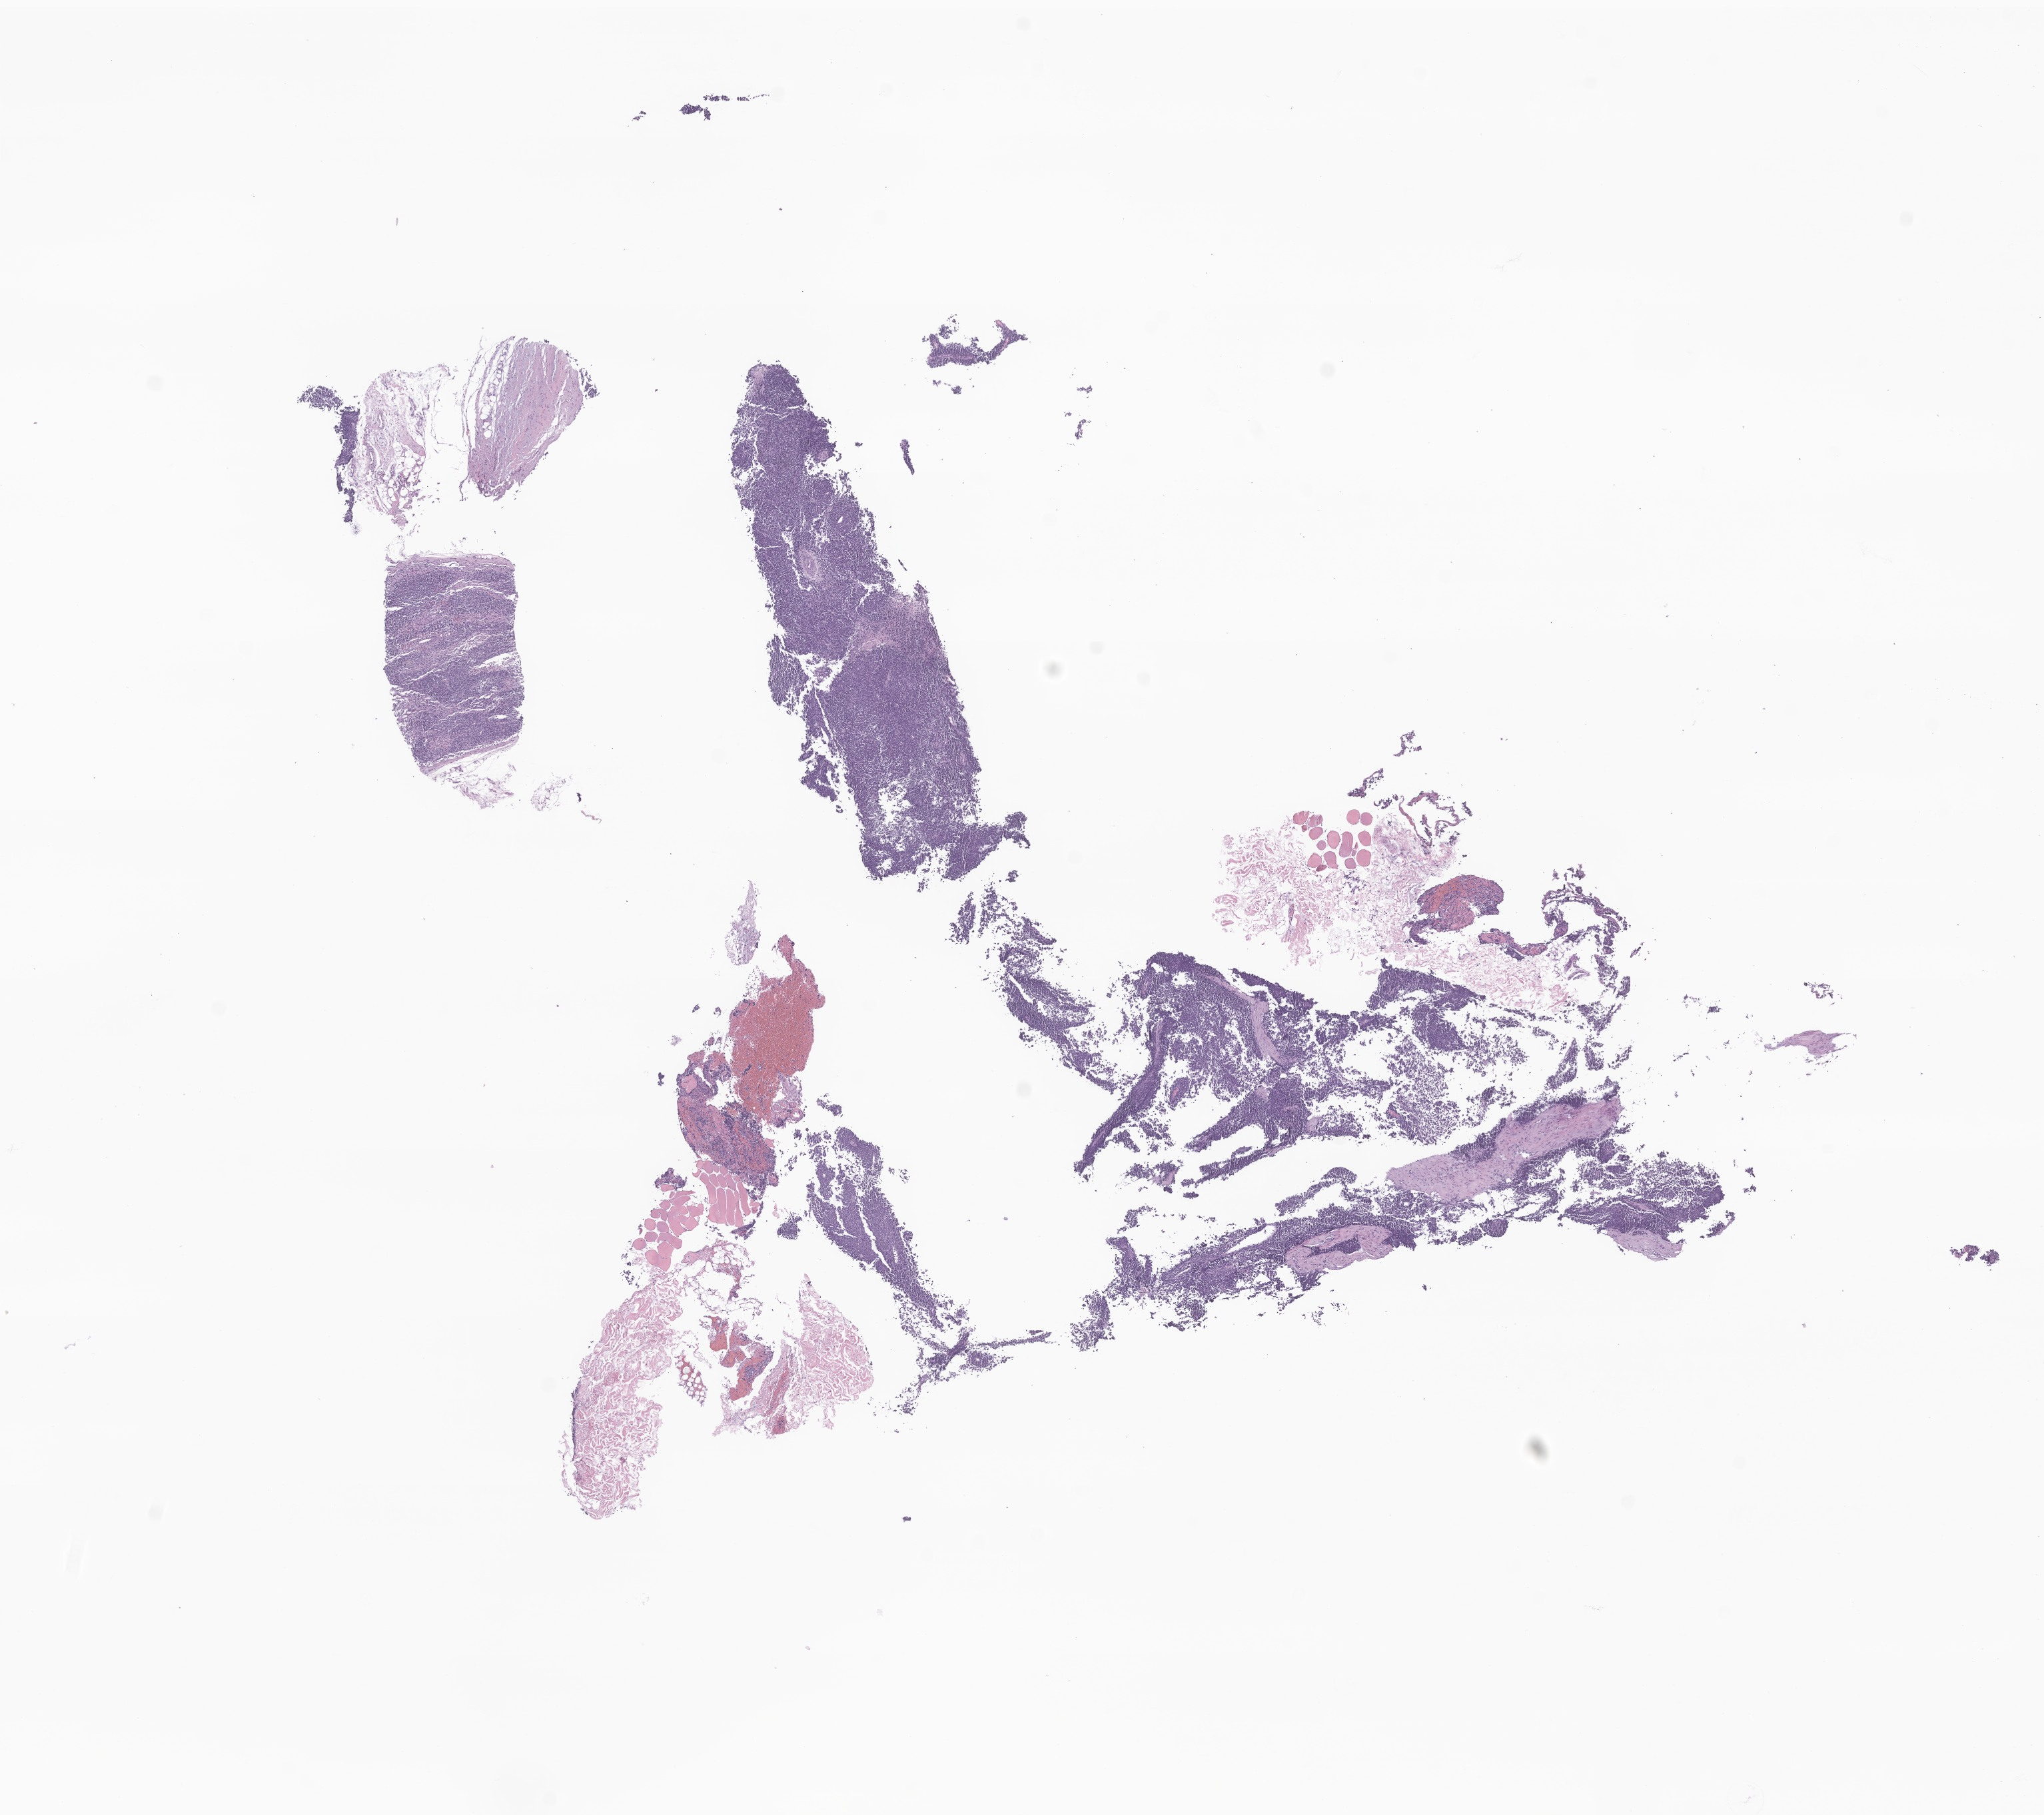
Digitized H&E-stained section of tumor tissue from the abdomen — whole scanned area (about 12.9 x 11.5 mm) shown as a low-resolution overview; formalin-fixed, paraffin-embedded (FFPE) tissue. Patient male; age 253 months (21 years 1 month).
Diagnosis (ICD-O-3 morphology term): Desmoplastic small round cell tumor.